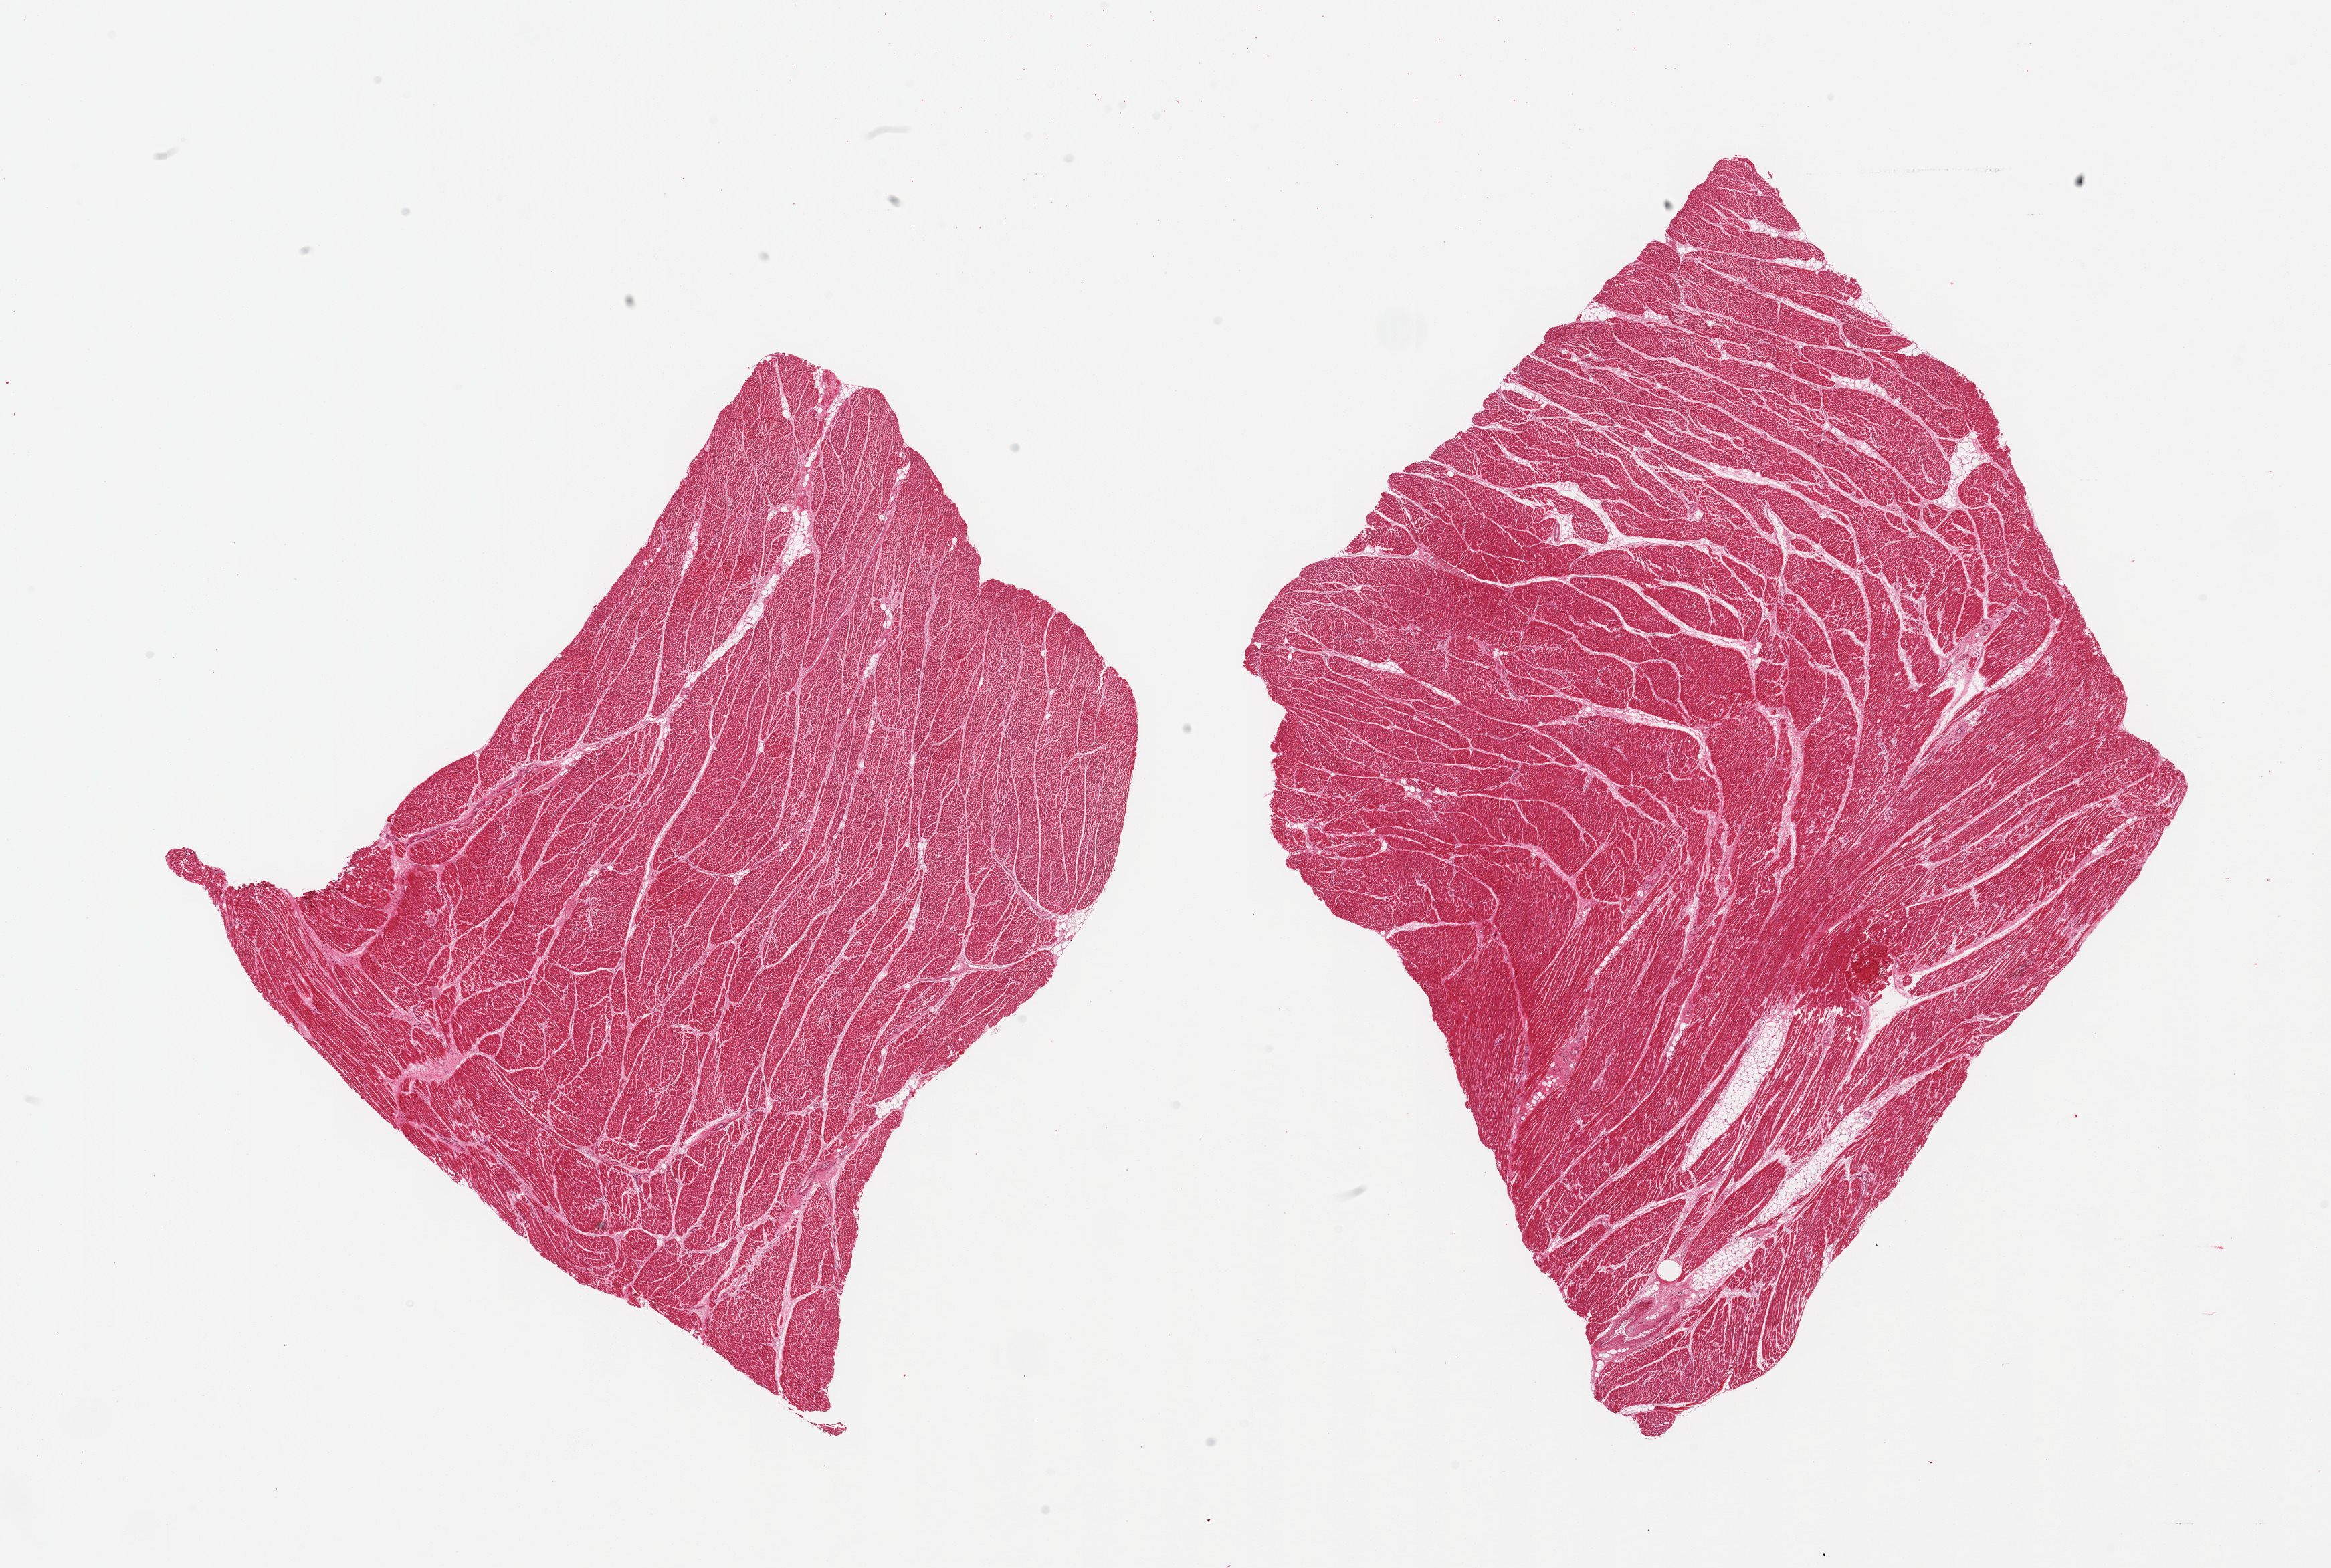
Whole-slide image, hematoxylin and eosin (H&E) stain — whole scanned area (about 27.6 x 18.5 mm) shown as a low-resolution overview; PAXgene-fixed, paraffin-embedded tissue; section of heart (target tissue); tissue donor sample. Donor: male.
• reviewer comment on this tissue sample: 2 pieces, moderate interstitial fibrosis/chronic ischemic changes